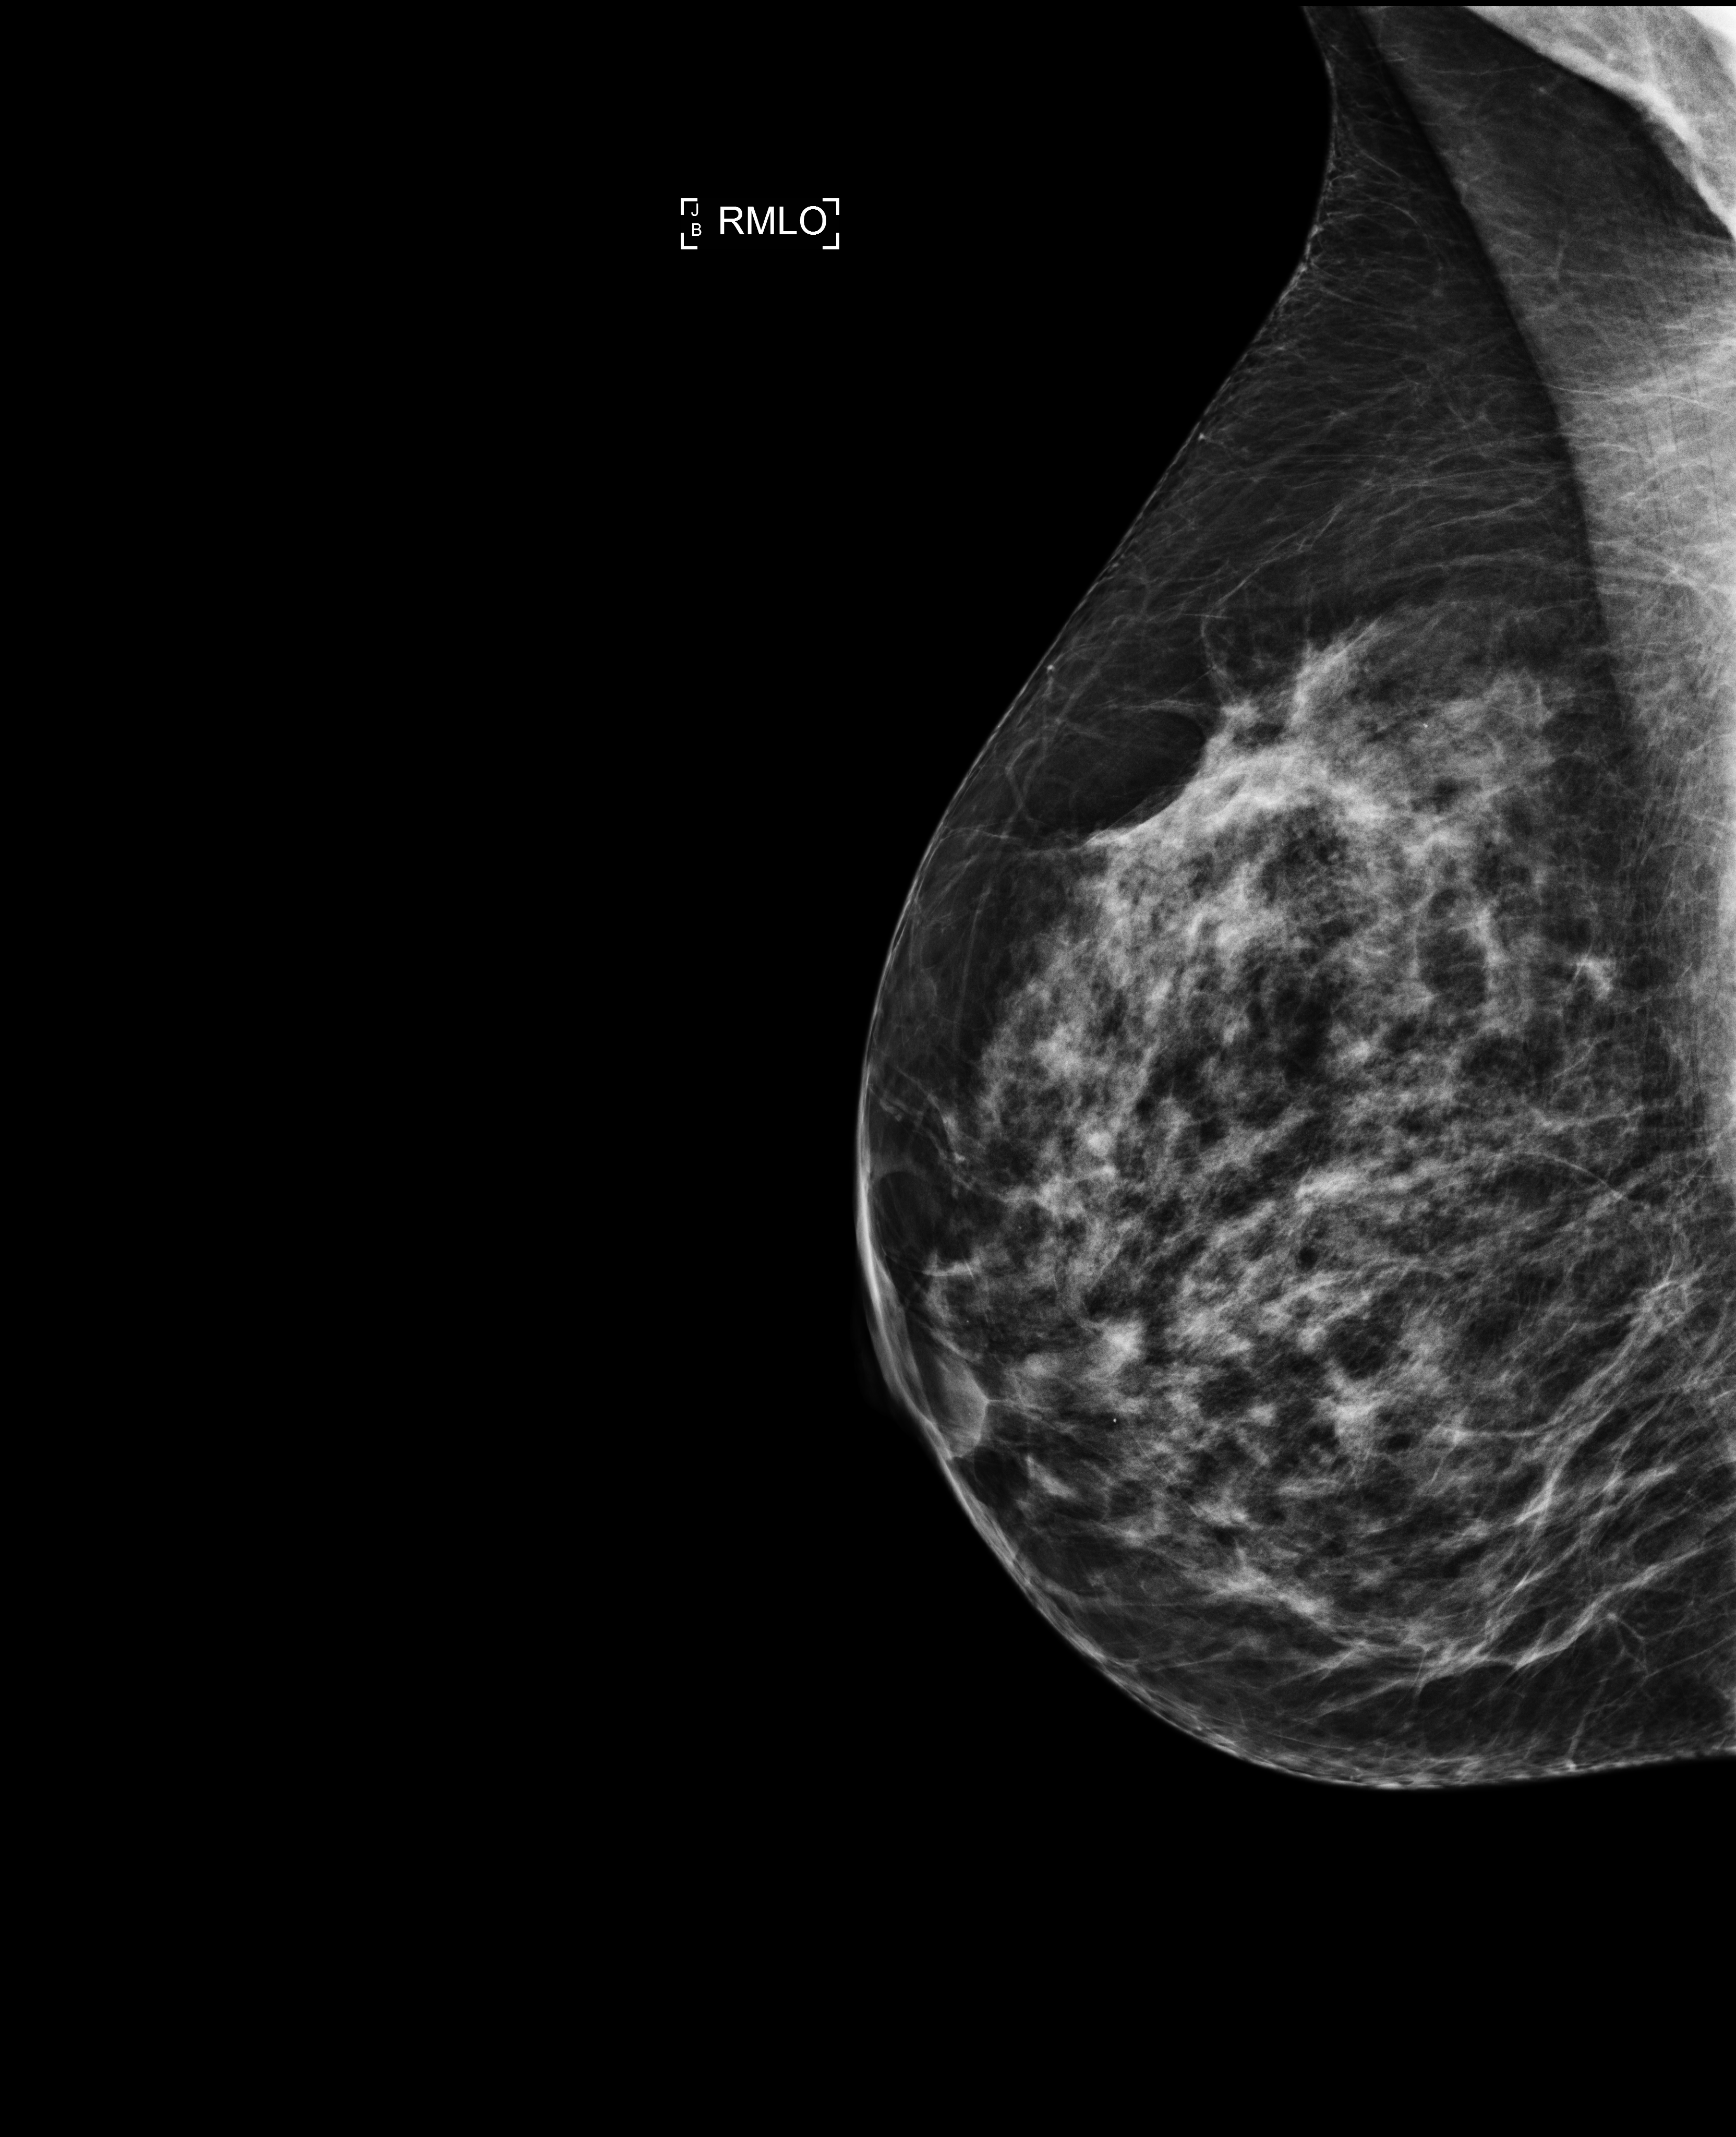
Digital mammogram (FFDM); right breast; mediolateral oblique (MLO) view; annual screening mammography examination; compressed breast thickness 82 mm. Patient: female, 47 years.
BI-RADS breast density category at the screening exam (both breasts, scale 1–4): 3. Final BI-RADS assessment for this screening round (tomosynthesis exam, both breasts): category 1. Recall: no recall after this screen.